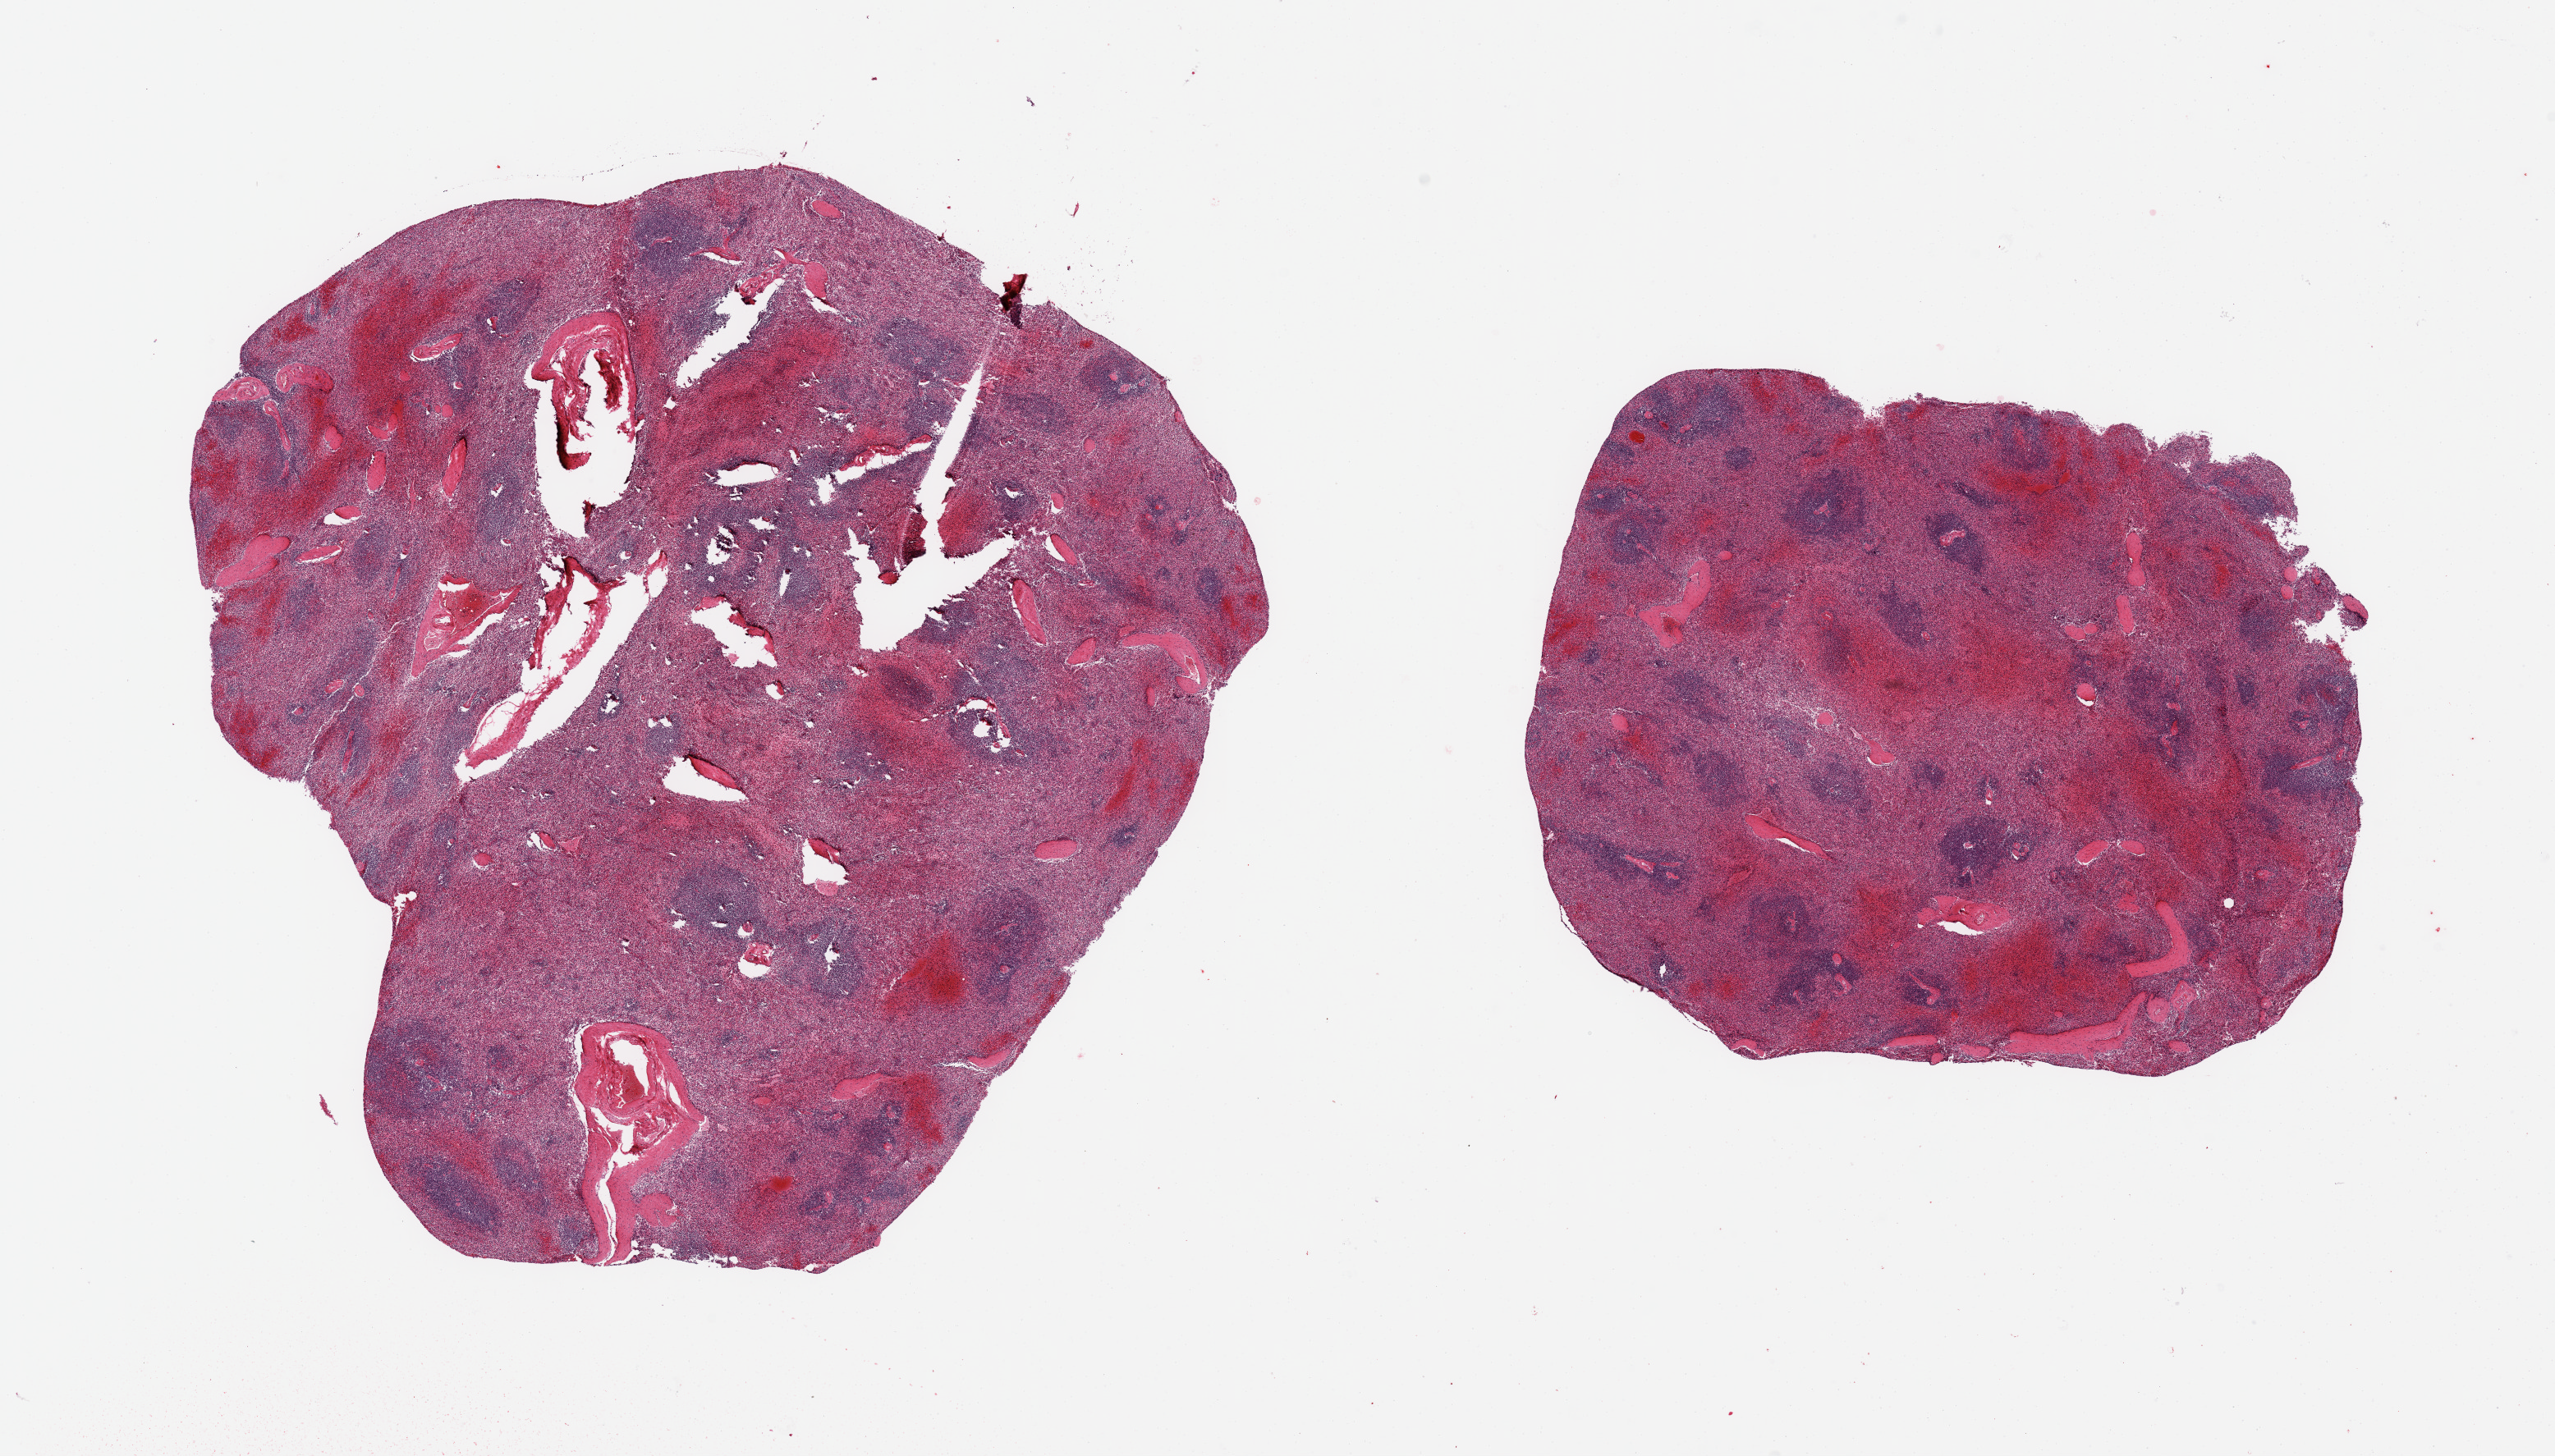
Digitized haematoxylin and eosin-stained section — a low-resolution overview of the entire scanned area, about 24.6 x 14.0 mm, PAXgene-fixed, paraffin-embedded tissue, section of spleen (target tissue), donor tissue sample. Donor: female.
• review note (as recorded): 2 pieces, moderate congestion & autolysis